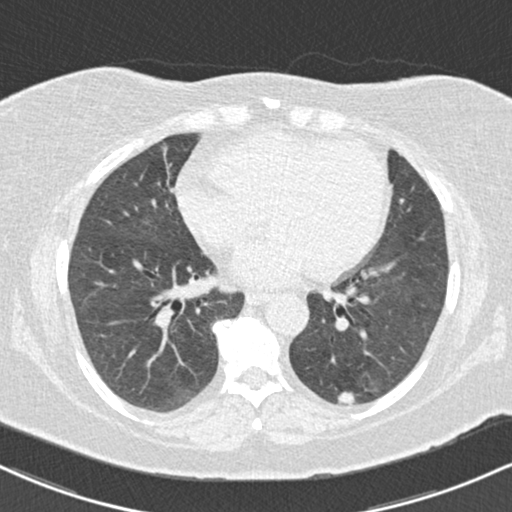
Low-dose screening chest CT, one axial slice. Position 68 of 147 along the scan axis. Lung window (W 1500 / L -600 HU). 2 mm slice thickness. 512 × 512 image matrix, field of view 322 × 322 mm.
Annotated regions visible in this slice (manually delineated by an expert):
- lesion 1 (tumor, lower lobe of left lung): box from (x=338, y=392) to (x=356, y=404) px